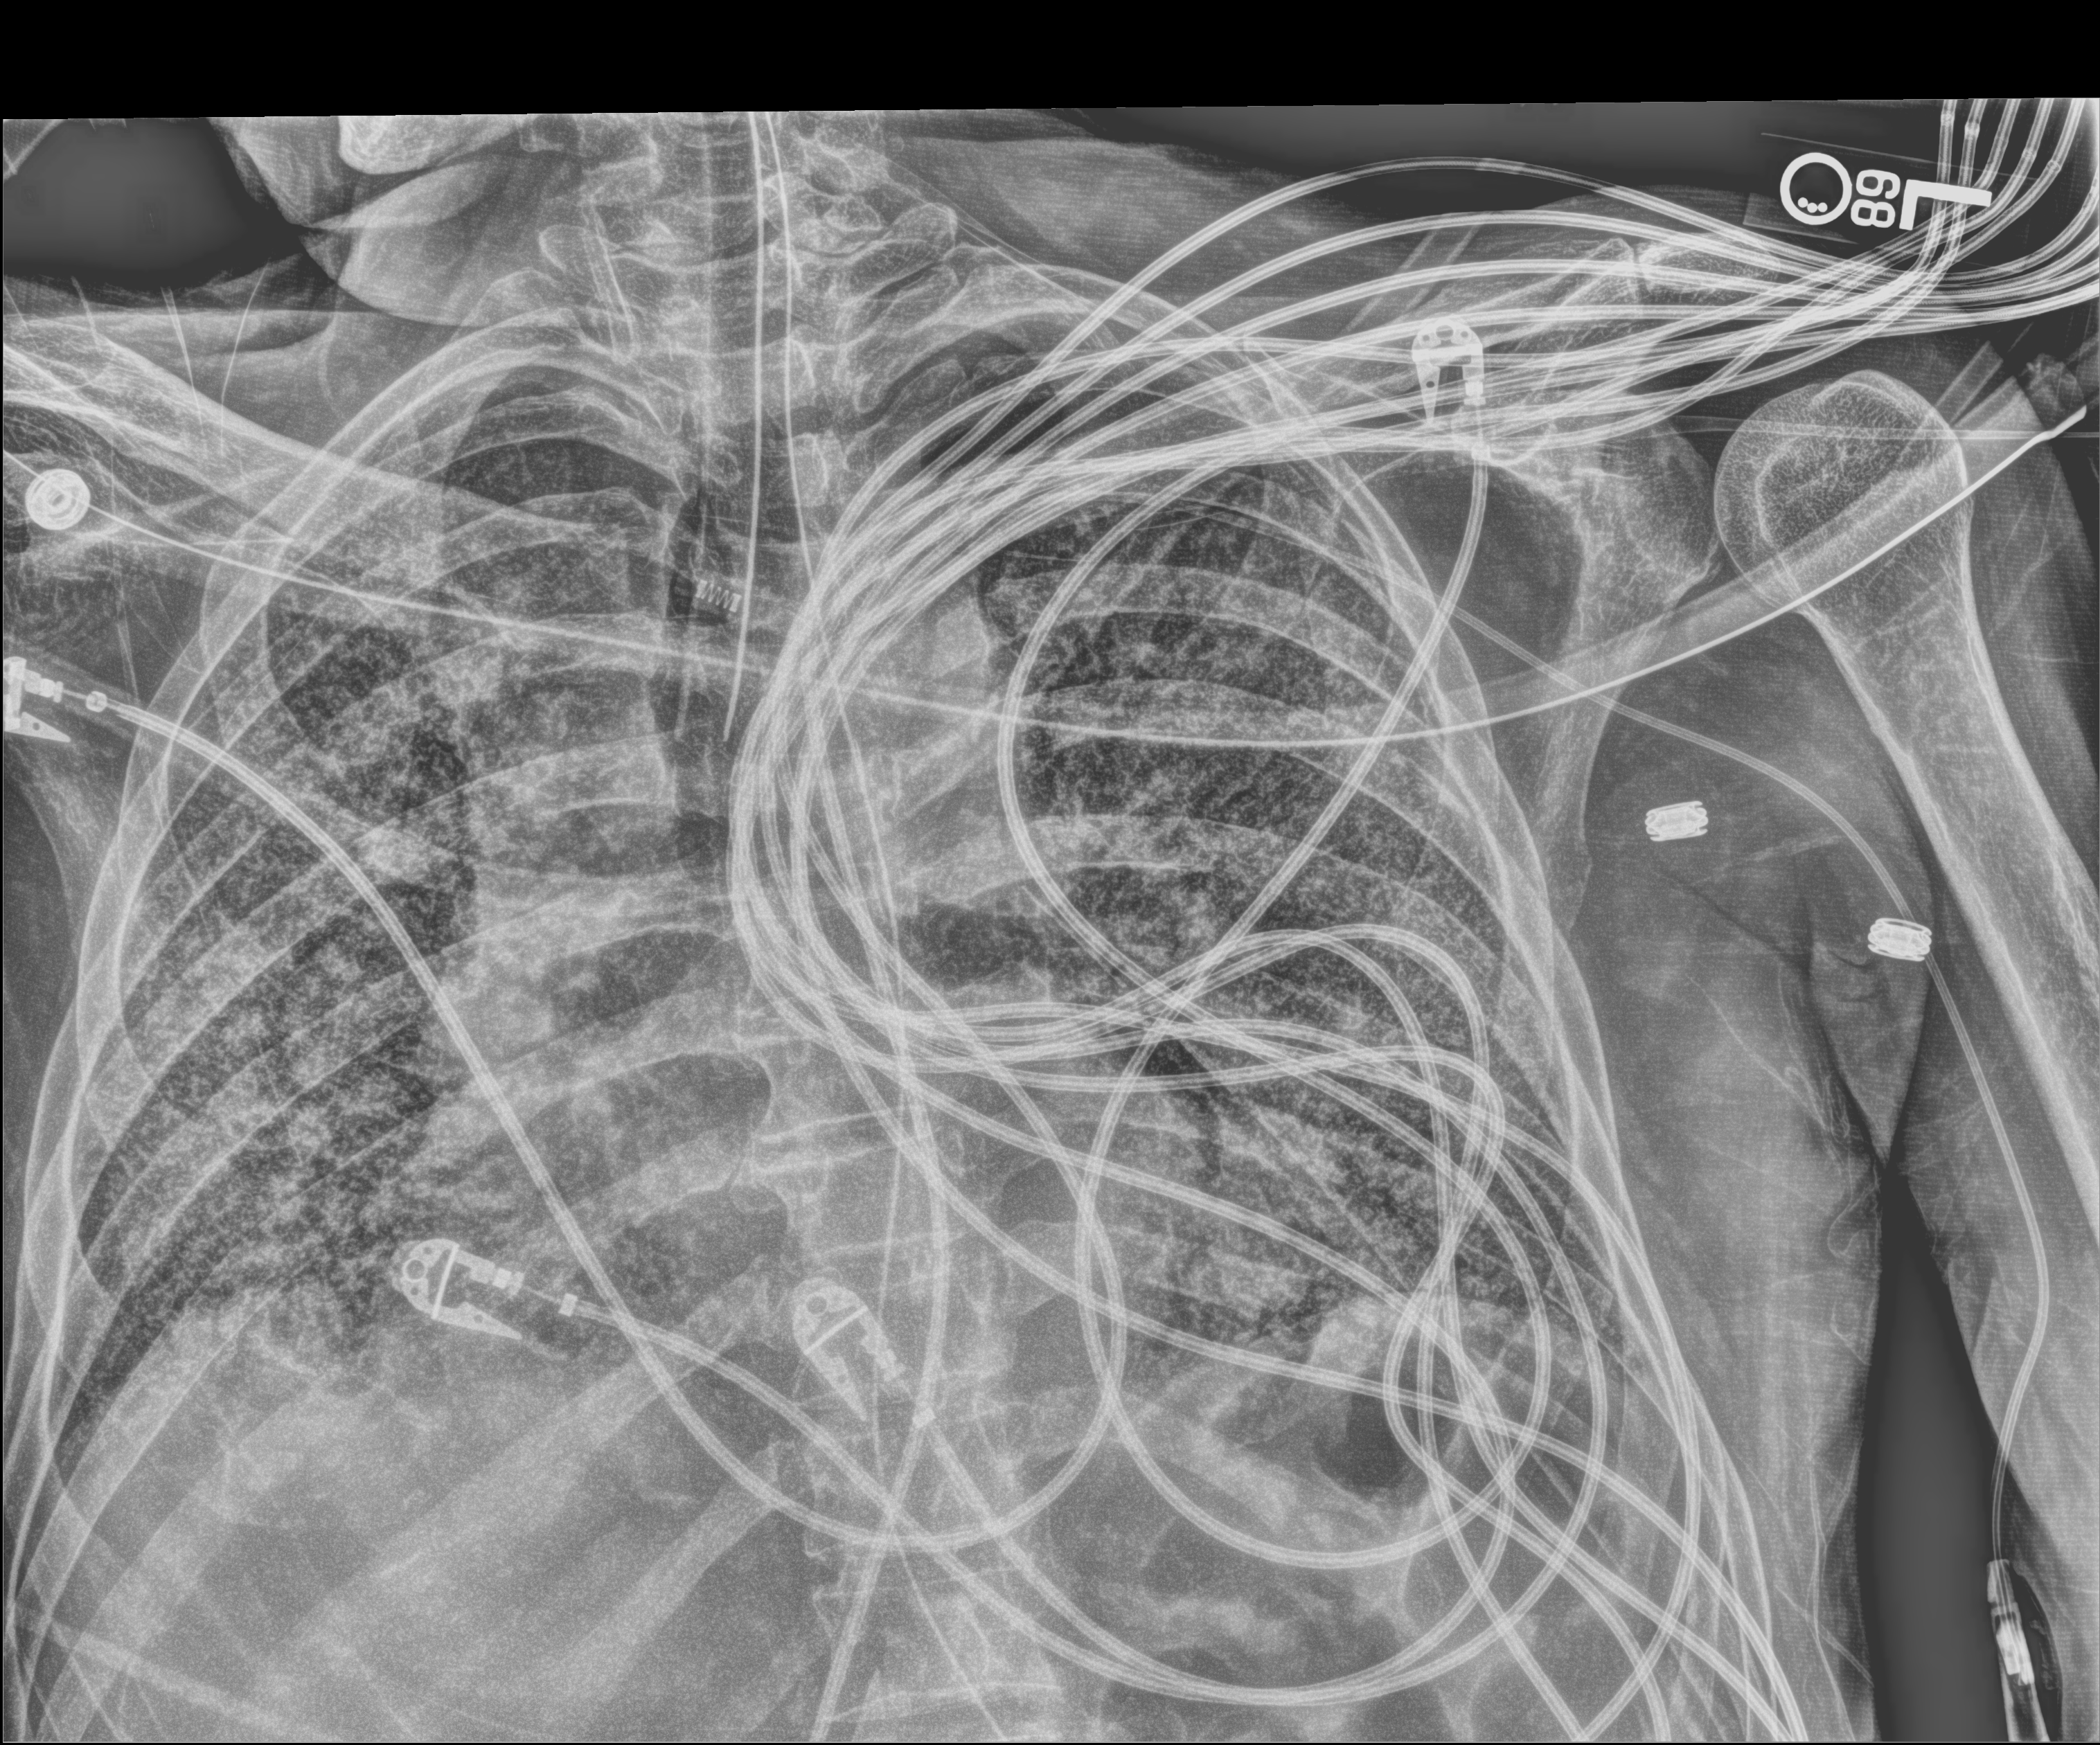
Chest X-ray (portable), anteroposterior (AP) projection. Male patient hospitalised with COVID-19, age 60–74 years.
From the hospital-stay record, not from the radiograph (when in the stay this image was taken is not recorded): mechanically ventilated during this hospital stay: yes; admitted to intensive care during this hospital stay: yes.